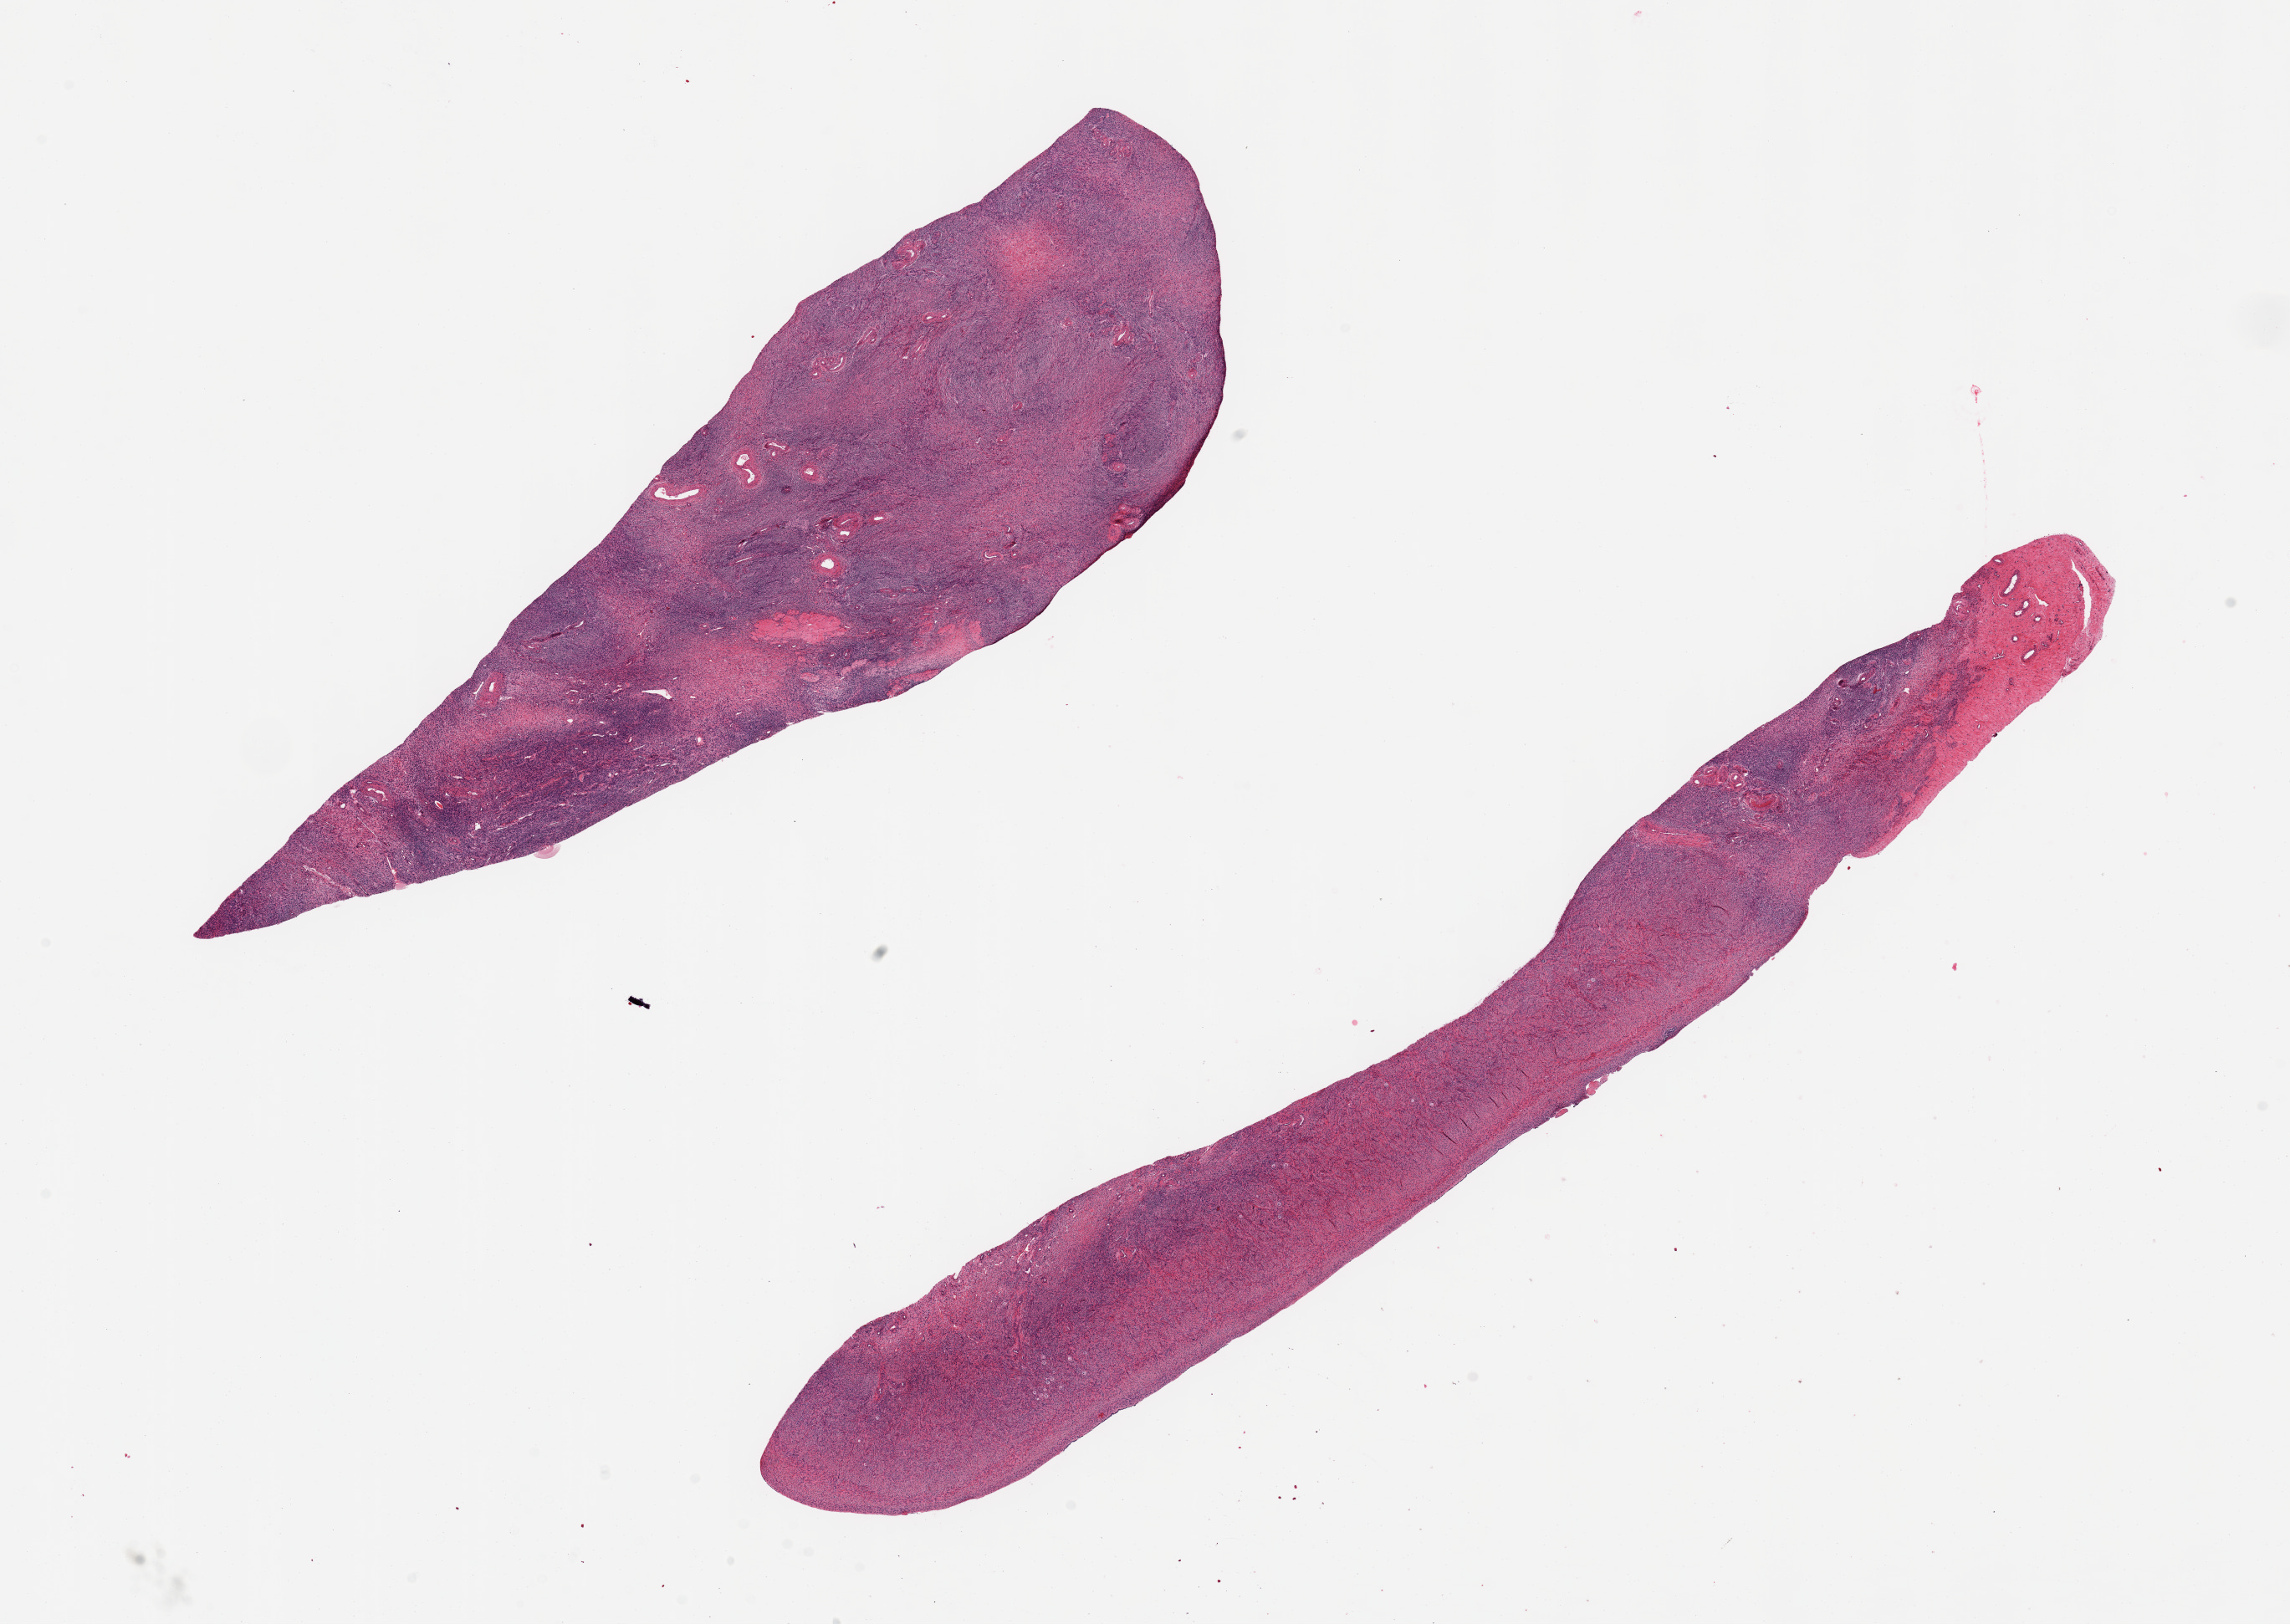
Haematoxylin and eosin whole-slide image, brightfield, a low-resolution overview of the entire scanned area, about 21.7 x 15.4 mm (acquisition: 20x scan), PAXgene-fixed paraffin-embedded (PFPE) section, target tissue: ovary, tissue donor sample. Female donor.
* review note (as recorded): 2 pieces, 15x2mm & 11x3 mm; ova and corpora